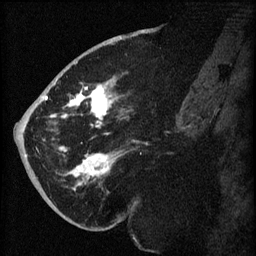
Breast MRI (dynamic contrast-enhanced), one sagittal slice. Slice 33 of 60 in the series (ordered by position). Dynamic contrast-enhanced series, image 2 of 3 at this slice position (ordered by acquisition). 1.5 T. TE 4.2 ms, TR 8.2 ms. 2 mm slice thickness. 256 × 256 image matrix. Patient: female, 71 years.
Outlined on this slice (semi-automatically segmented with operator editing):
- analysis volume of interest (the breast-tissue region the enhancement analysis was run in; not a lesion): bounding box <40,72,139,196> (left, top, right, bottom; pixels)
- tumour enhancement mask (voxels above the 70 % enhancement threshold inside the analysis volume of interest): <42,83,134,191>